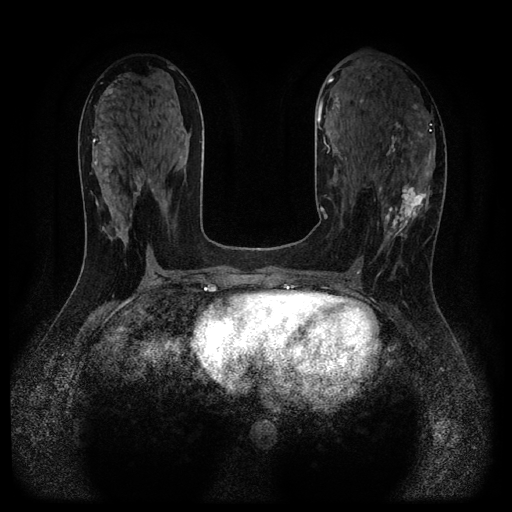
Breast MRI (dynamic contrast-enhanced, multi-phase), one axial slice. Position 53 of 116 along the scan axis. Dynamic contrast-enhanced series, time point 2 of 5 at this slice position (early post-contrast). 1.5 T. TE 2.7 ms, TR 5.4 ms. 2.2 mm slice thickness. 512 × 512 image matrix, field of view 330 × 330 mm. Patient: female, 43 years.
Outlined on this slice (semi-automatic segmentation, software-assisted and operator-edited):
- breast lesion (labelled 'tumour' in the annotation; benign lesions carry a separate 'benign' label): bounding box (x1, y1, x2, y2) in pixels: (378, 181, 432, 251)